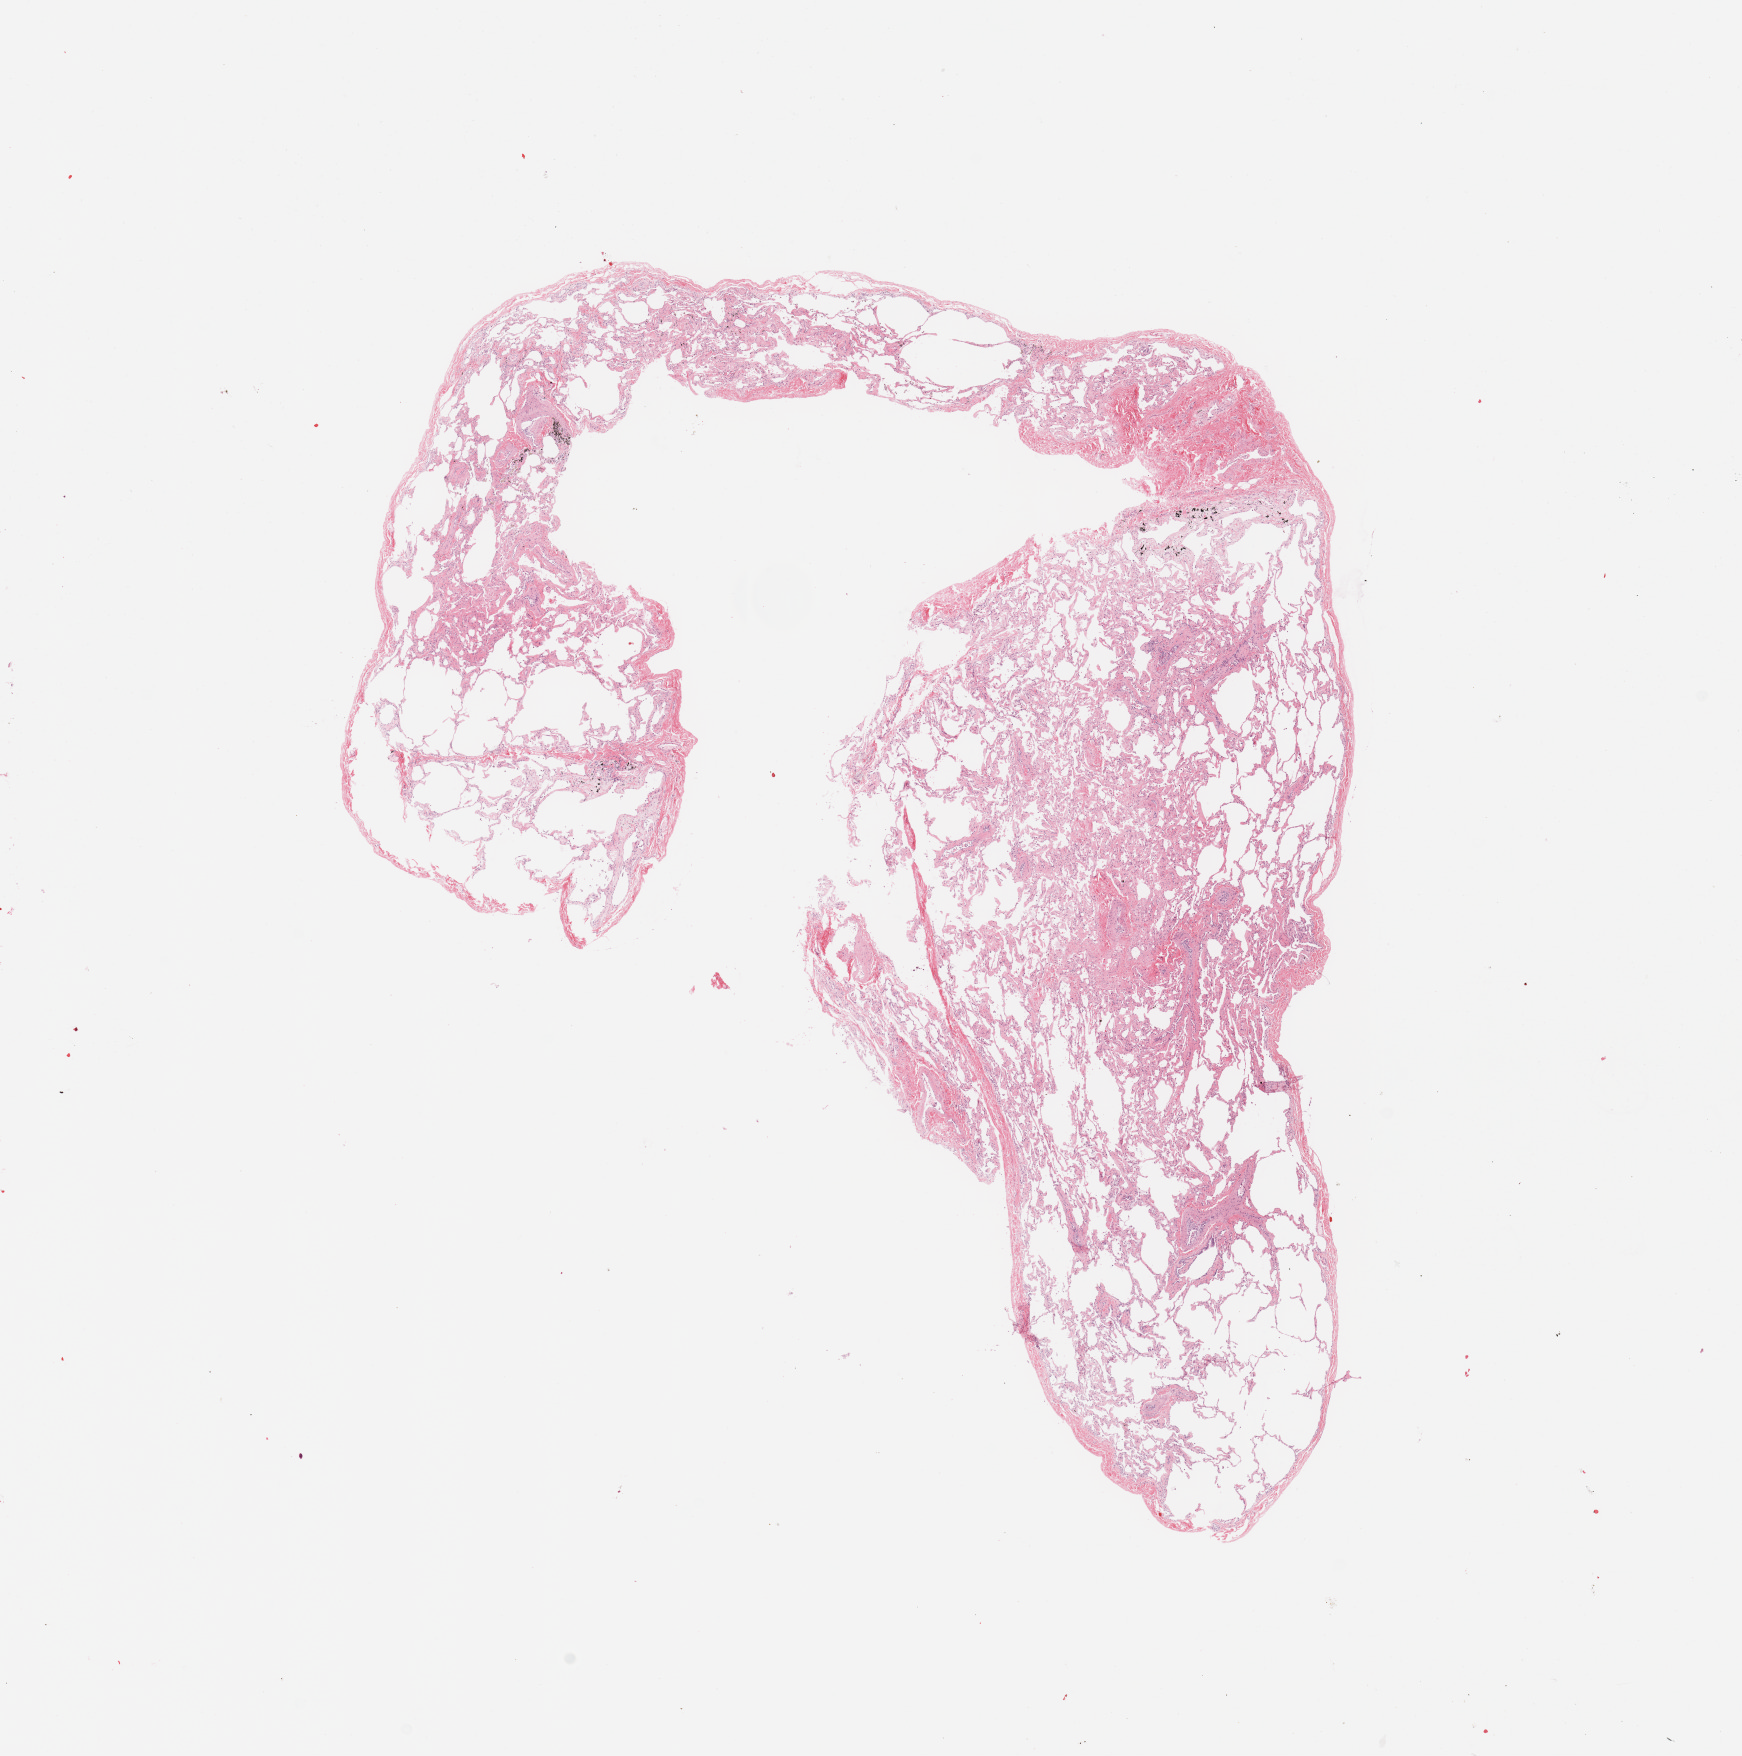
Hematoxylin and eosin (H&E) stained whole-slide image, a low-resolution overview of the entire scanned area, about 13.8 x 13.9 mm. Lung, normal (non-tumour) tissue. Male, 62 y/o.
This section: normal (non-tumour) tissue from the same patient. Patient diagnosis: Squamous cell carcinoma, NOS.